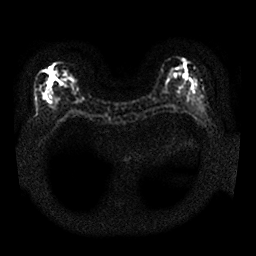
Breast MRI, one axial slice; slice 6 of 25 in the series (ordered by position); diffusion-weighted series; image 2 of 4 stored at this slice position (different b-values; order by instance number); 1.5 T; 4 mm slice thickness; 256 × 256 image matrix, field of view 340 × 340 mm. Female patient.
Annotated regions visible in this slice (expert manual segmentation):
- tumour on diffusion-weighted imaging: bounding box [x1, y1, x2, y2] px = [45, 67, 52, 86]